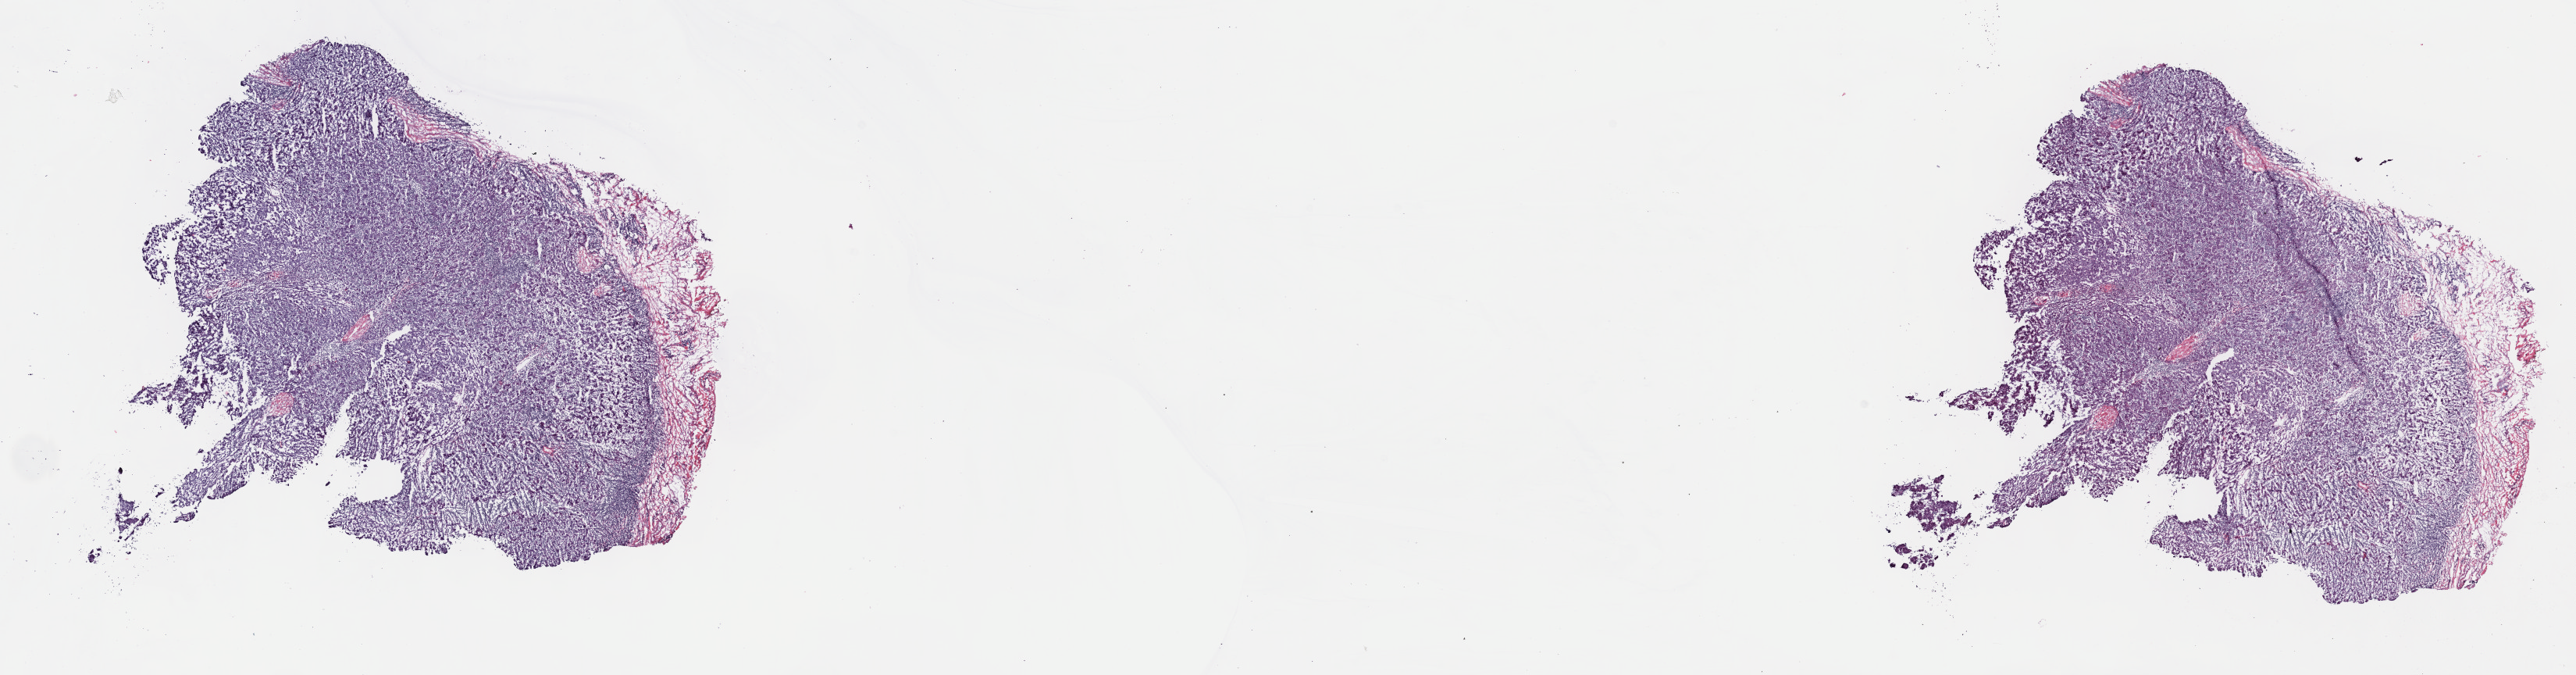
Hematoxylin and eosin (H&E) stained whole-slide image, shown as a low-resolution overview of the whole scanned area (about 26.7 x 7.0 mm, from a 40x scan). Frozen section. Thymus, primary tumour sample. Female, age 61 years at initial diagnosis. Slide review estimates, as recorded: tumour cells 85%, tumour nuclei 85%, normal cells 0%, stromal cells 15%, necrosis 0%. Inflammatory infiltration, as recorded: lymphocyte infiltration 1%, monocyte infiltration 1%, neutrophil infiltration 1%.
Diagnosis: Thymoma, type B3, malignant.